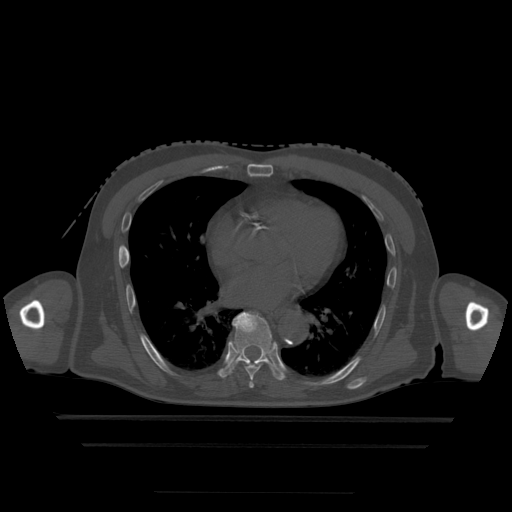
CT including the spine, one axial slice; position 289 of 522 along the scan axis; bone window (W 1800 / L 400 HU); 1.25 mm slice thickness; 512 × 512 image matrix, field of view 436 × 436 mm. Patient age 68 years. From the clinical record (not read from this slice): primary cancer: urothelial.
Outlined on this slice (semi-automatically segmented with operator editing):
- T6 vertebra: box from (x=249, y=380) to (x=254, y=389) px
- T7 vertebra: (x=246, y=364)–(x=261, y=381)
- T8 vertebra: (x=221, y=313)–(x=284, y=381)